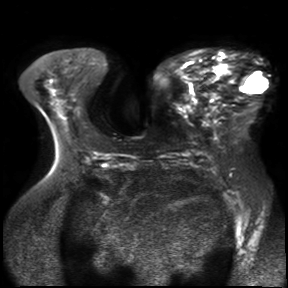
Breast MRI, one axial slice. Slice 15 of 30 in the series (ordered by position). Diffusion-weighted series; image 2 of 4 stored at this slice position (different b-values; order by instance number). 3 T. 288 × 288 image matrix, field of view 360 × 360 mm. Female patient.
Outlined on this slice (manually delineated by an expert):
- tumour on diffusion-weighted imaging: box from (x=217, y=64) to (x=231, y=77) px